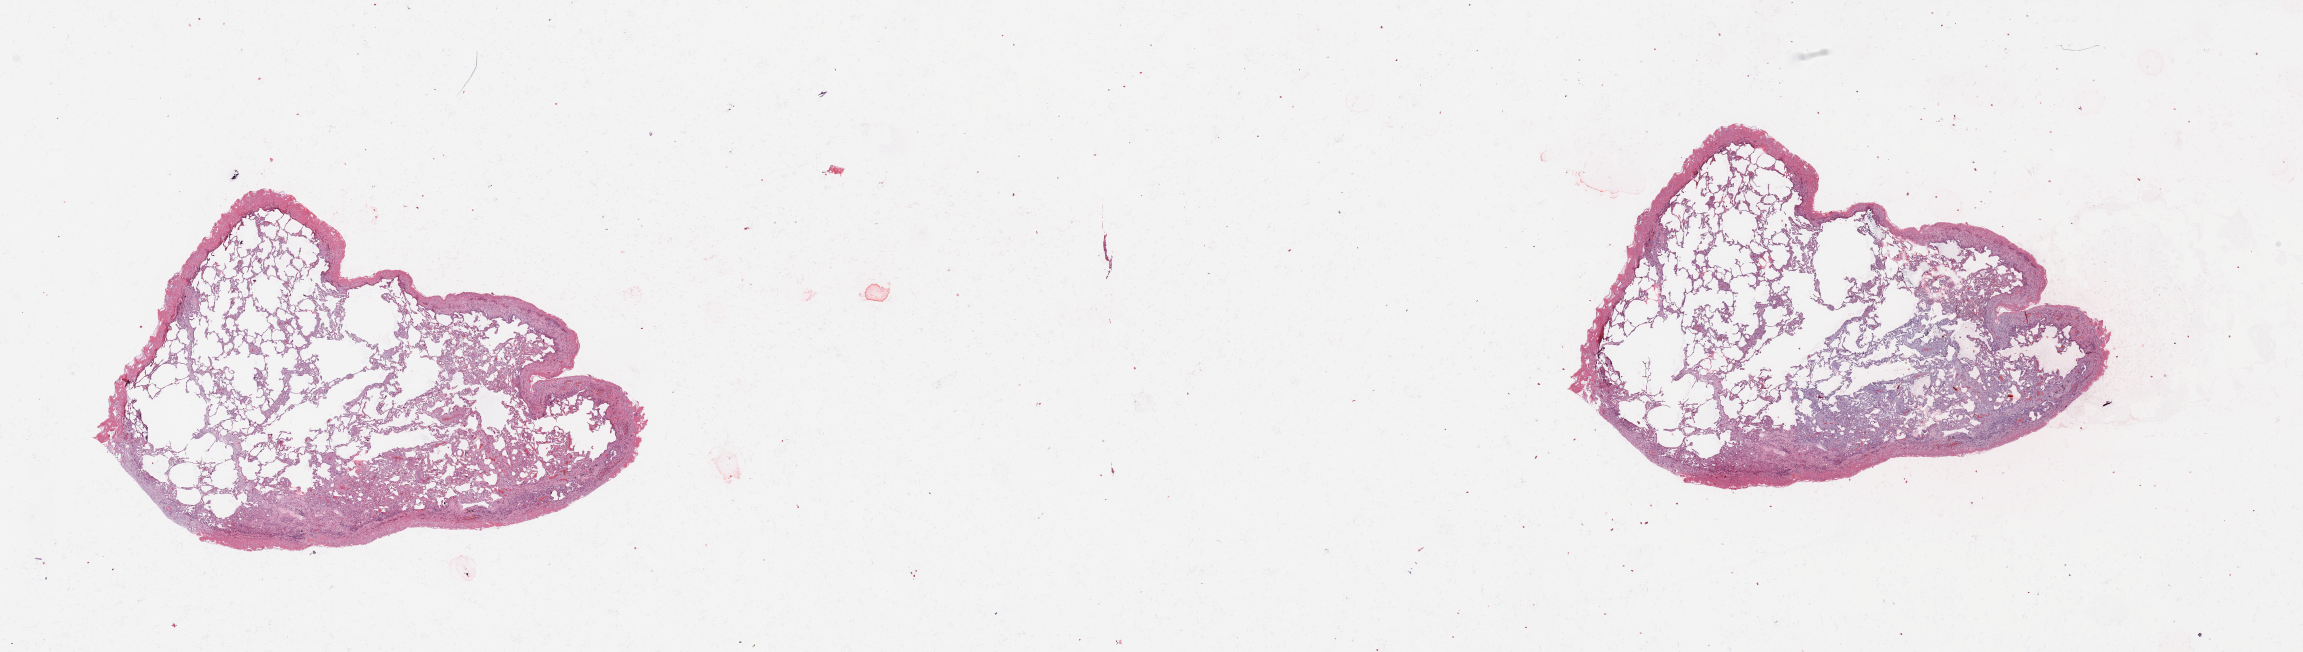
Digitized H&E tissue section (whole slide), low-resolution overview of the scanned area, about 36.4 x 10.3 mm; normal (non-tumour) tissue sample, sampled site: lung. Patient: male, age 57 years.
This section: normal (non-tumour) tissue from the same patient. Patient diagnosis: Squamous cell carcinoma, NOS.